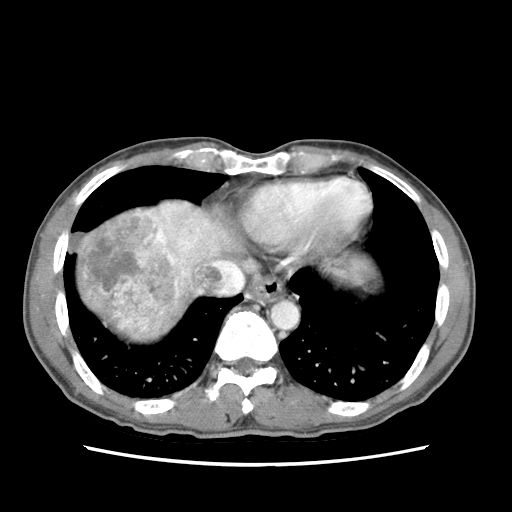
Contrast-enhanced abdominal CT (liver protocol), one axial slice. Slice 67 of 79 in the series (ordered by position). Reconstruction kernel STANDARD. Soft-tissue window (W 400 / L 40 HU). 512 × 512 image matrix, field of view 320 × 320 mm. Case-level facts recorded for this patient, not image findings: diagnosis: hepatocellular carcinoma (patient treated with transarterial chemoembolisation; whether this scan precedes or follows treatment is not stated here); TNM stage (as recorded): Stage-IIIB; Child-Pugh class: A; tumour differentiation: moderately differentiated.
Annotated regions visible in this slice (semi-automatically segmented with operator editing):
- abdominal aorta: bounding box (x1, y1, x2, y2) in pixels: (272, 301, 297, 328)
- liver parenchyma outside the tumour (the mass and vessels are separate outlines, so this box may not span the whole liver): (72, 196, 248, 344)
- mass: (77, 202, 192, 337)
- liver vessels: (160, 204, 215, 250)